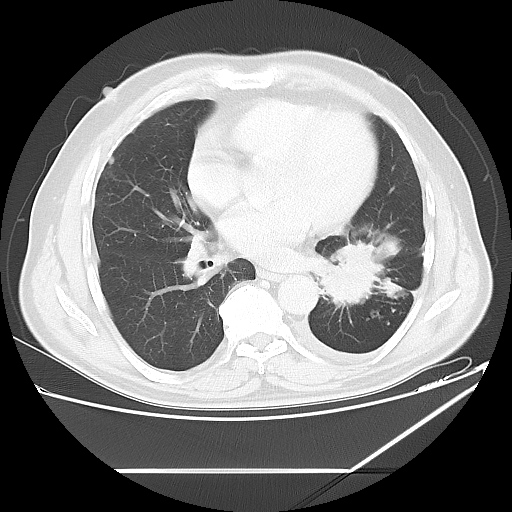
Chest CT, one axial slice; slice 27 of 60 in the series (ordered by position); lung window (W 1500 / L -600 HU); 5 mm slice thickness; 512 × 512 image matrix, field of view 395 × 395 mm. Male patient, age 62 years. From the clinical record (not read from this slice): clinical TNM (as recorded): T3 N0 M1.
Structures marked on this image (rectangle marked by the reading radiologist):
- lung tumour (recorded histology: adenocarcinoma): bounding box [x1, y1, x2, y2] px = [320, 236, 408, 310]
- lung tumour (recorded histology: adenocarcinoma): [328, 239, 387, 308]